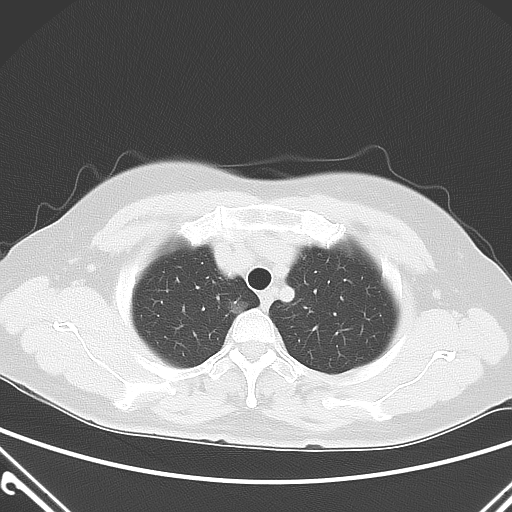
Chest CT, one axial slice; slice 48 of 60 in the series (ordered by position); lung window (W 1500 / L -600 HU); 5 mm slice thickness; 512 × 512 image matrix. Female patient, age 54 years. From the clinical record (not read from this slice): clinical TNM (as recorded): T1a N0 M0; histopathological grade: G1.
Outlined on this slice (rectangle marked by the reading radiologist):
- lung tumour (recorded histology: adenocarcinoma): bounding box <228,295,251,324> (left, top, right, bottom; pixels)